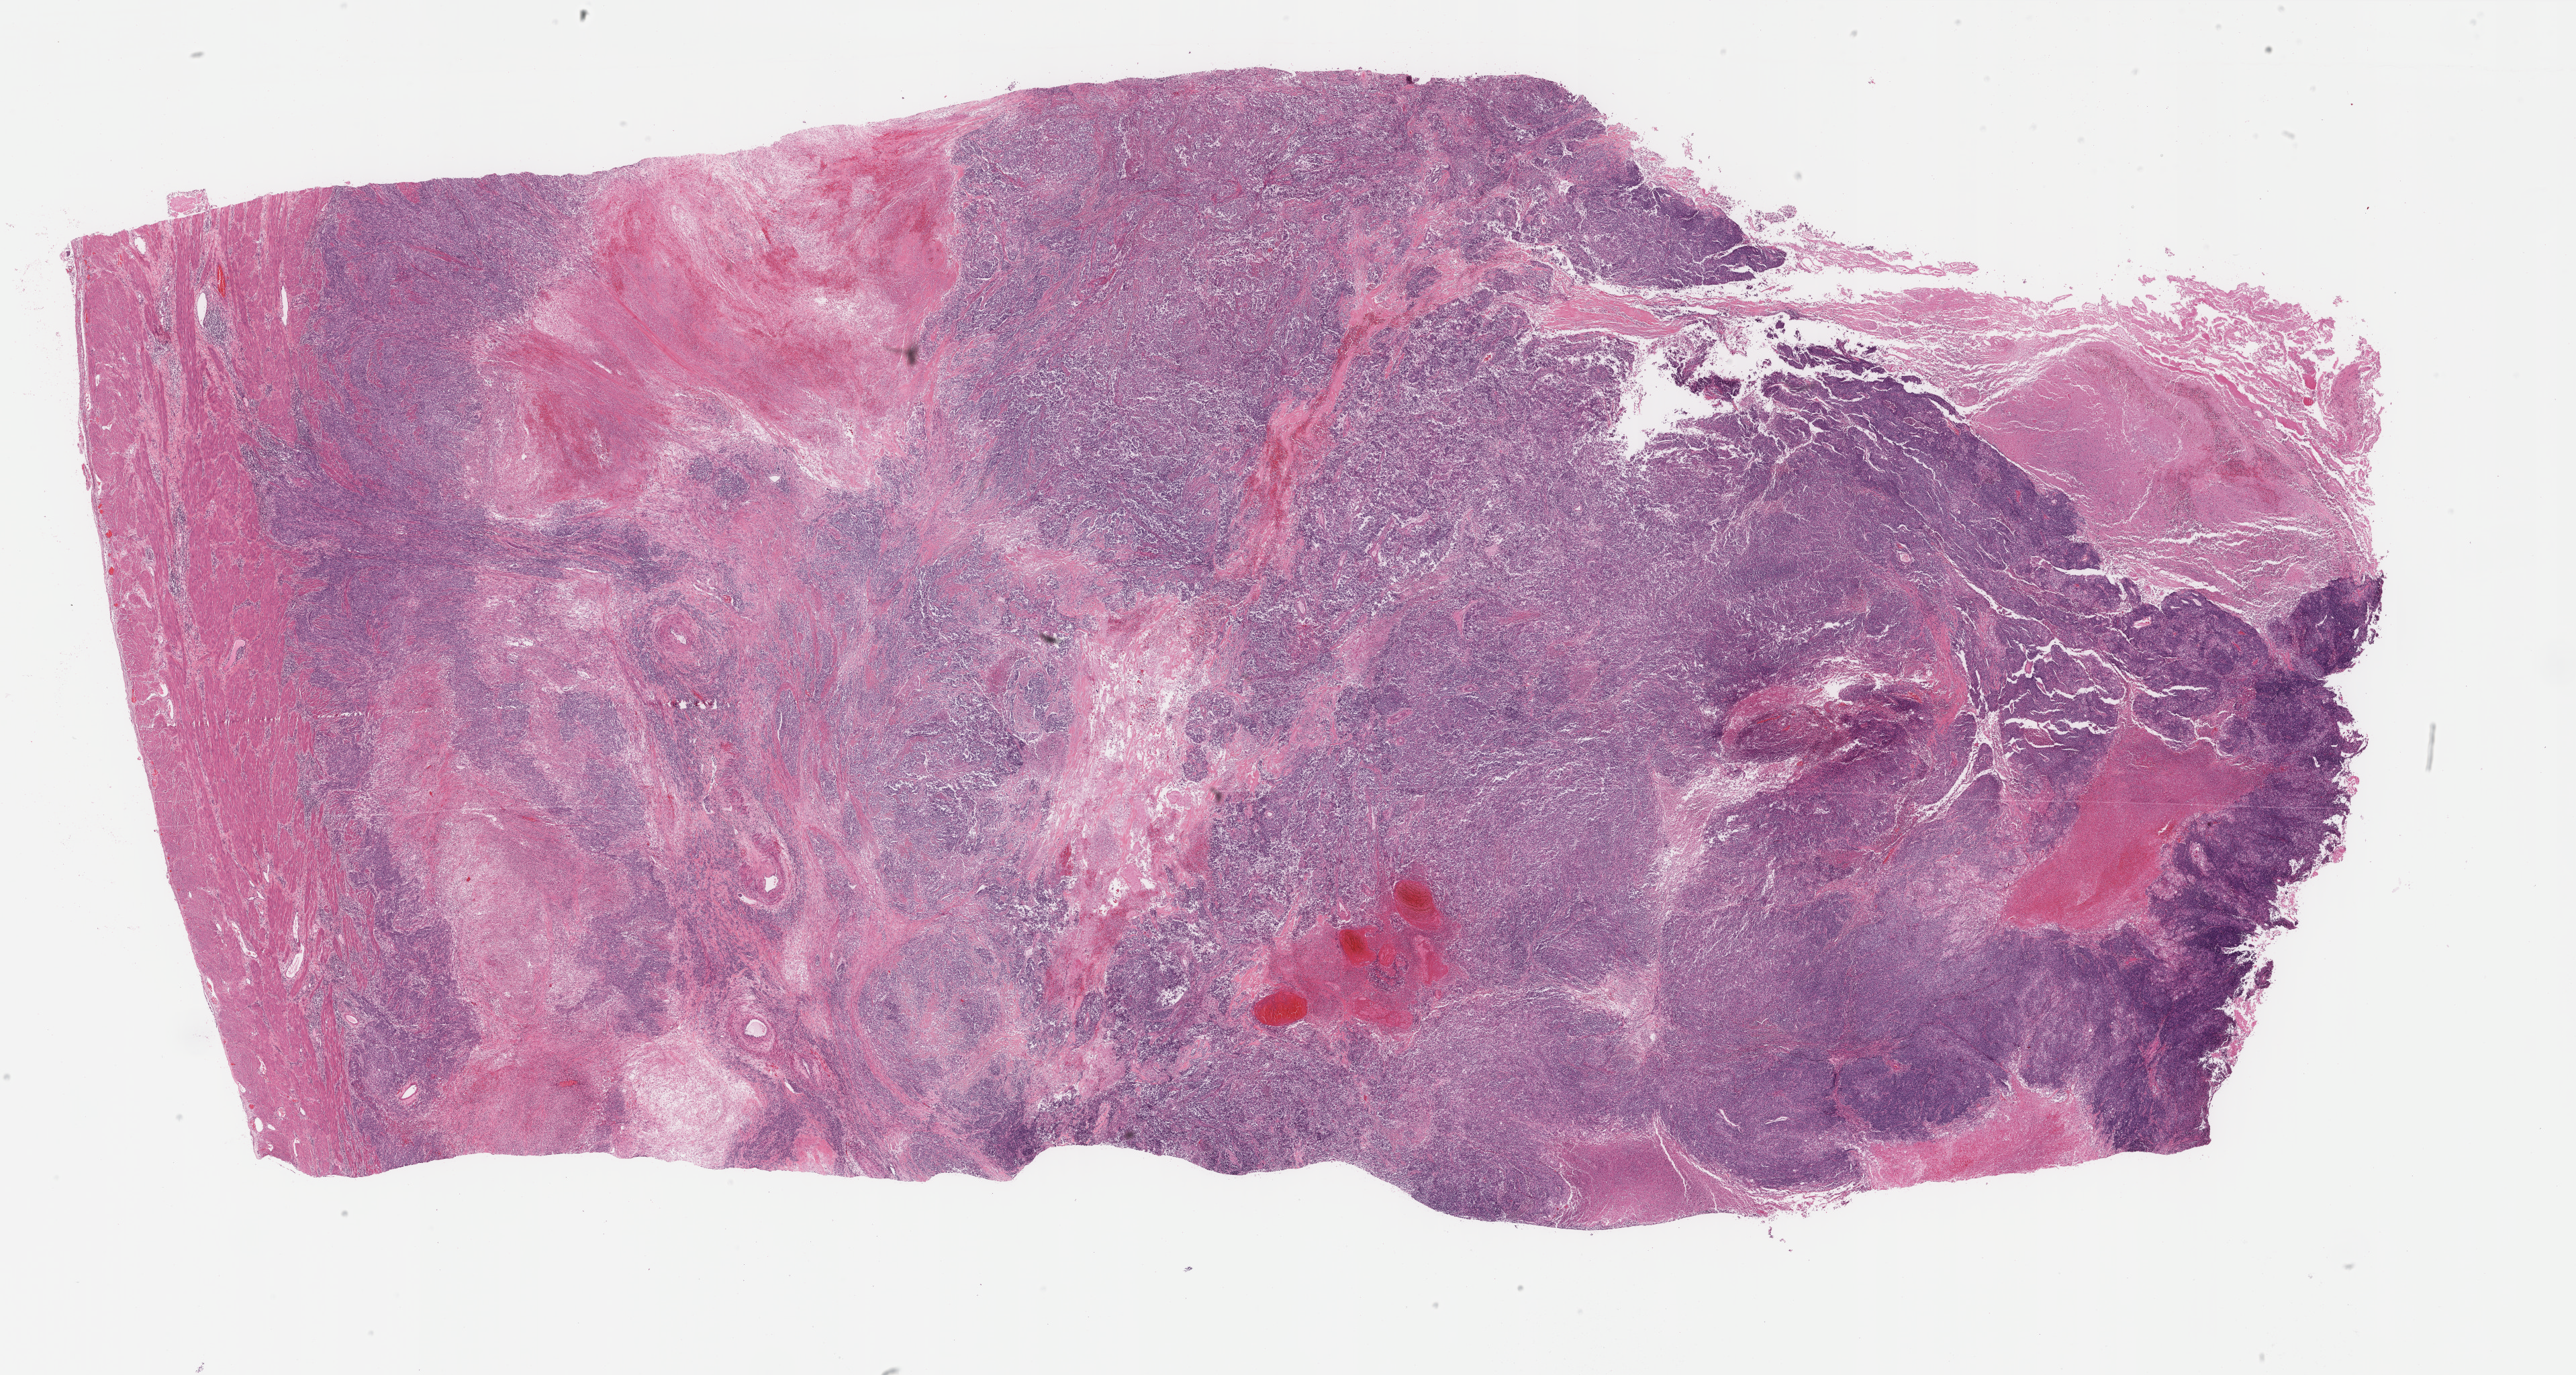
H&E whole-slide image, whole scanned area (about 30.5 x 16.3 mm, from a 40x scan) shown as a low-resolution overview; FFPE section; uterus, primary tumour sample. Female, age 47 years at initial diagnosis. Histologic grade: G3 (poorly differentiated).
Diagnosis: Endometrioid adenocarcinoma, NOS. FIGO stage: IIIC.